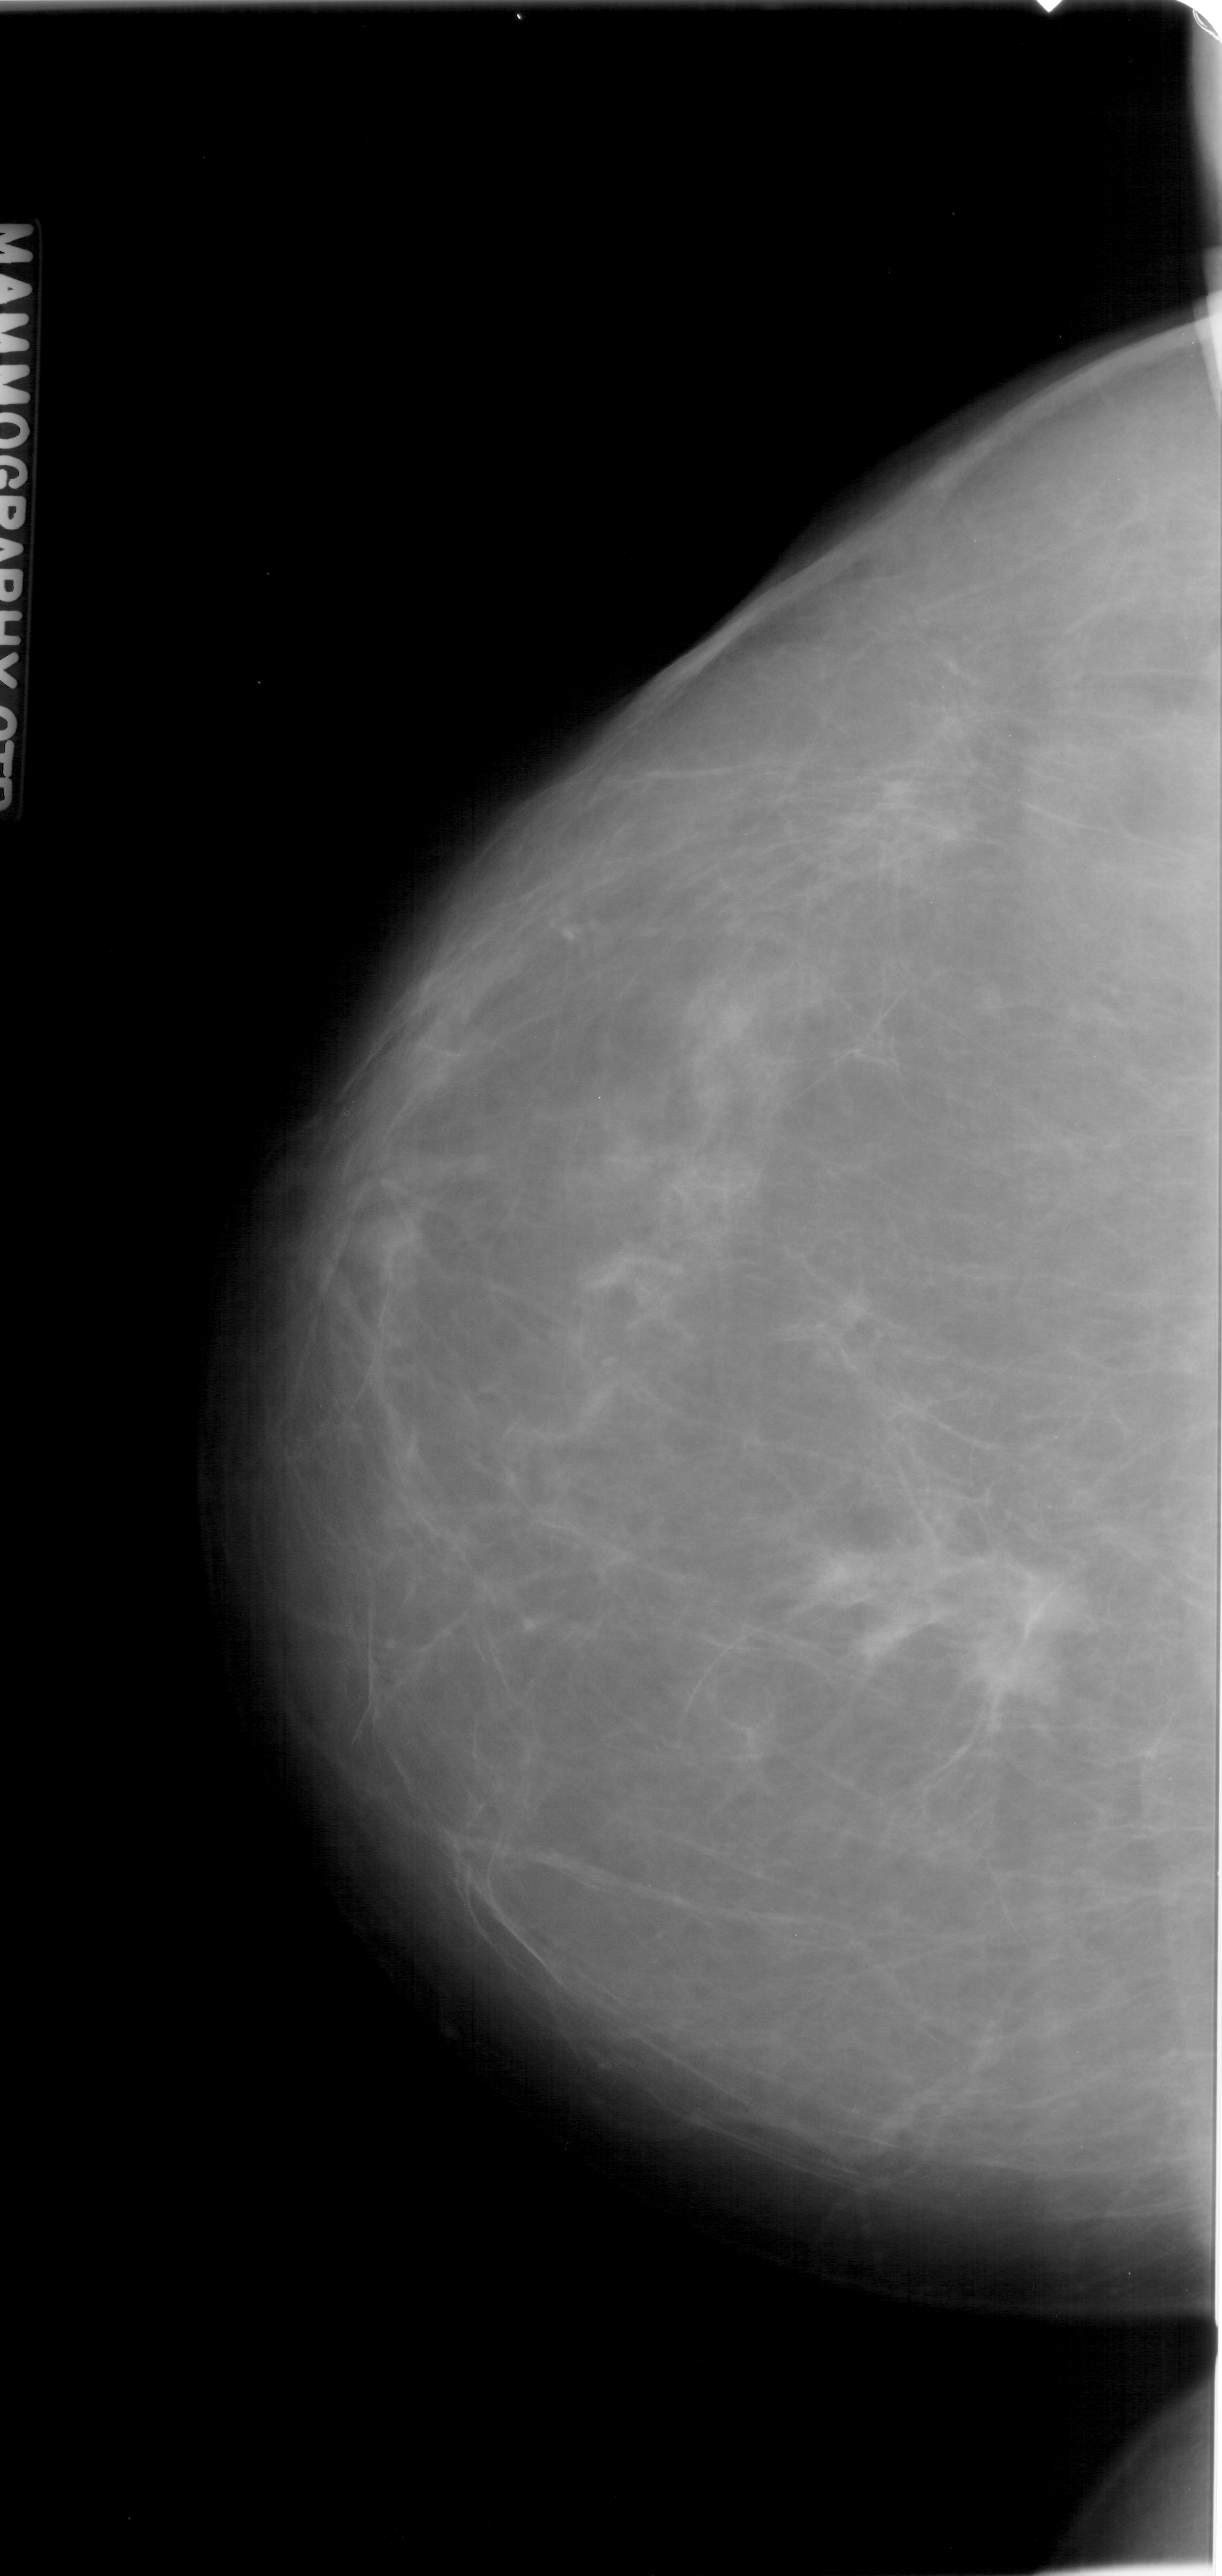
Digitized screen-film mammogram; left breast; CC view; BI-RADS breast density category 2 (scale 1–4); 1222 × 2576 image matrix.
Marked abnormalities (boxes around the expert regions of interest):
- mass, shape irregular, margins ill defined; BI-RADS assessment category 4; pathology (as recorded): malignant: bounding box [x1, y1, x2, y2] px = [878, 1516, 1110, 1688]